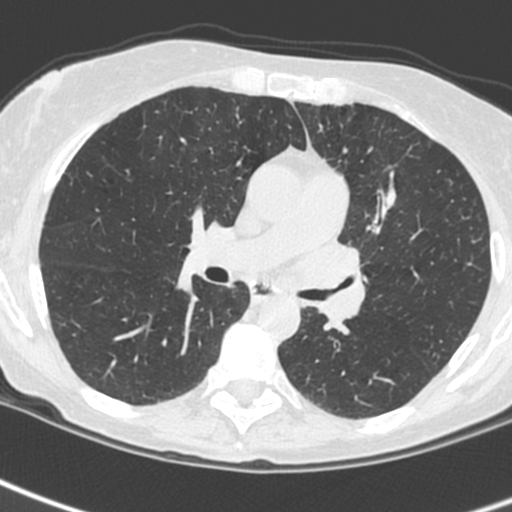
Low-dose screening chest CT, one axial slice. 120 kVp. Lung window (W 1500 / L -600 HU). 1.3 mm slice thickness. 512 × 512 image matrix, field of view 284 × 284 mm.
Annotated regions visible in this slice (manually delineated by an expert):
- lesion 3 (tumor, upper lobe of left lung): bounding box <293,235,366,322> (left, top, right, bottom; pixels)